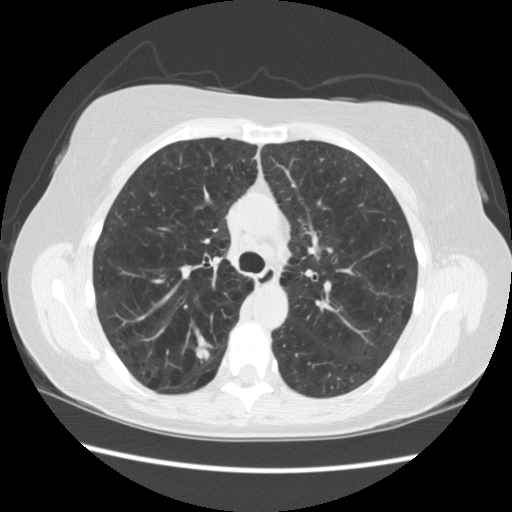
Chest CT (low-dose screening protocol), one axial image. Third annual screen. Lung window (W 1500 / L -600 HU). 2.5 mm slice thickness. 120 kVp. Slice 79 of 235 in the series. 512 × 512 image matrix. Female, age 55 years at enrolment. Current smoker at enrolment.
Expert-annotated lung lesion, box from (x=175, y=326) to (x=227, y=375) px. Reader record for this screening exam (exam-level; its link to the box is not recorded): non-calcified nodule or mass ≥4 mm, right upper lobe, 11 × 11 mm, poorly defined margins, soft tissue attenuation, pre-existing on the prior screen: no. Participant outcome: lung cancer diagnosed 96 days after this screen — small cell carcinoma, NOS, right upper lobe.